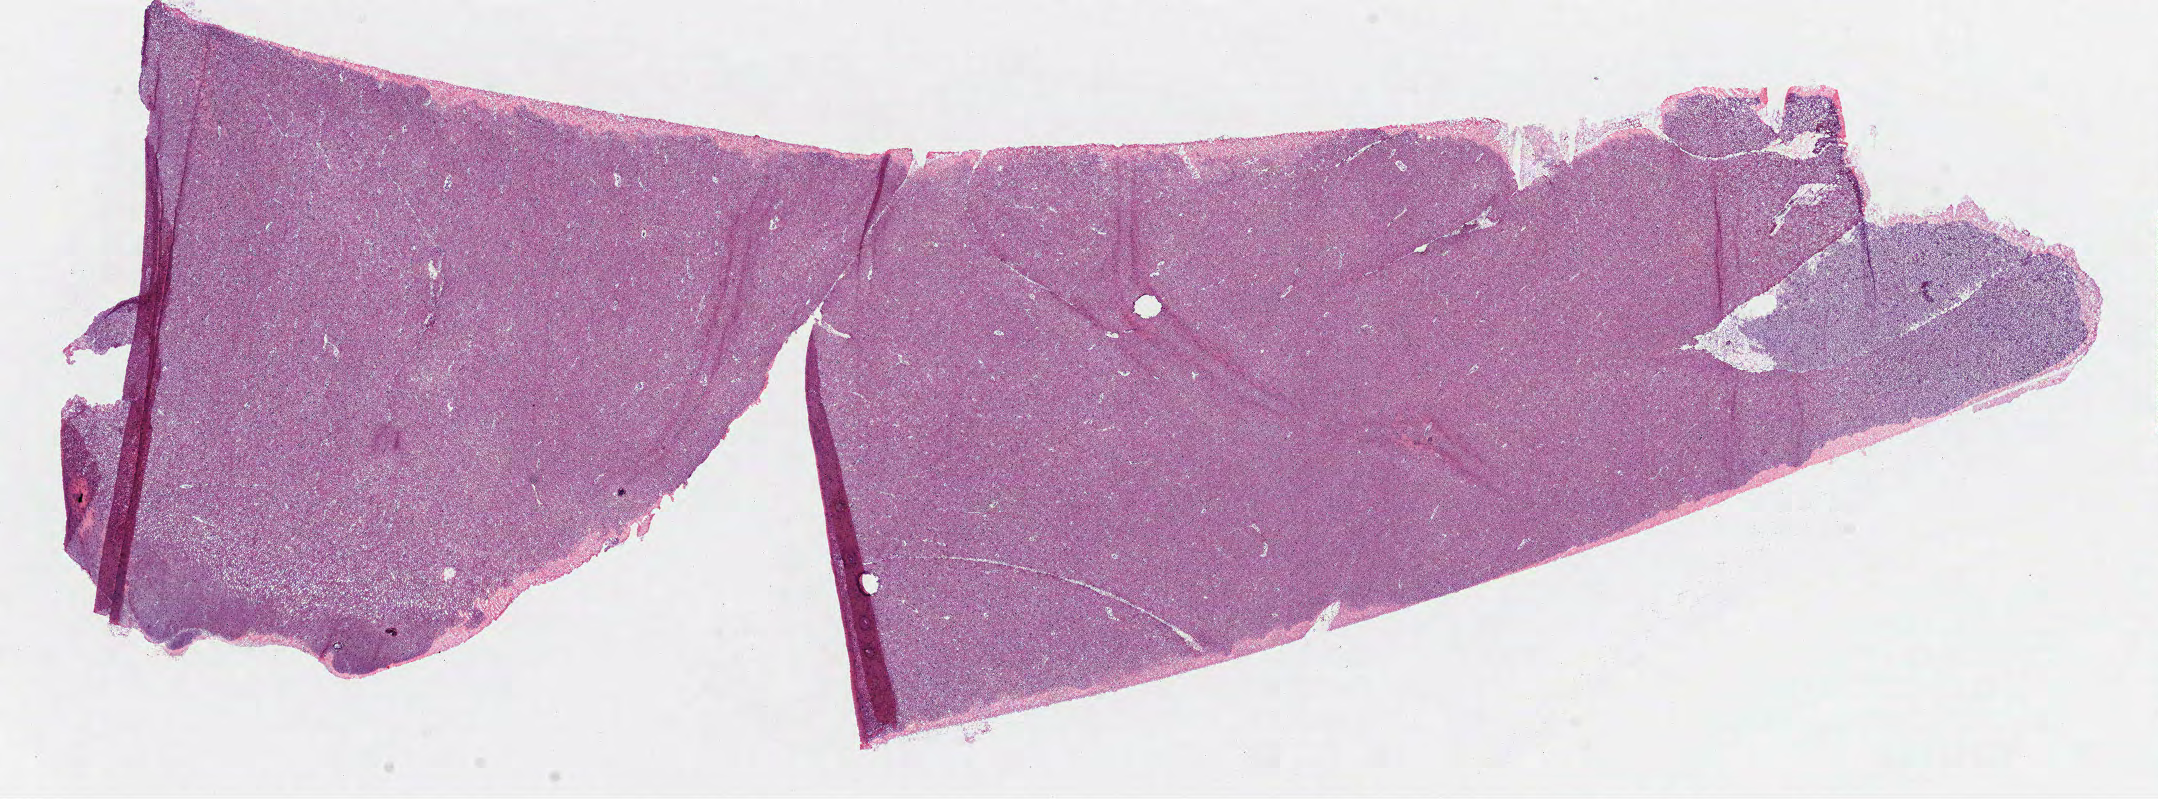
Whole-slide histology image, H&E-stained — shown as a low-resolution overview of the whole scanned area (about 17.4 x 6.4 mm, from a 40x scan), frozen section, brain, primary tumour sample. Male, age 40 years at initial diagnosis. Histologic grade: G3 (poorly differentiated). Slide review estimates, as recorded: tumour cells 95%, tumour nuclei 60%, normal cells 5%, stromal cells 0%, necrosis 0%.
* diagnosis: Oligodendroglioma, anaplastic